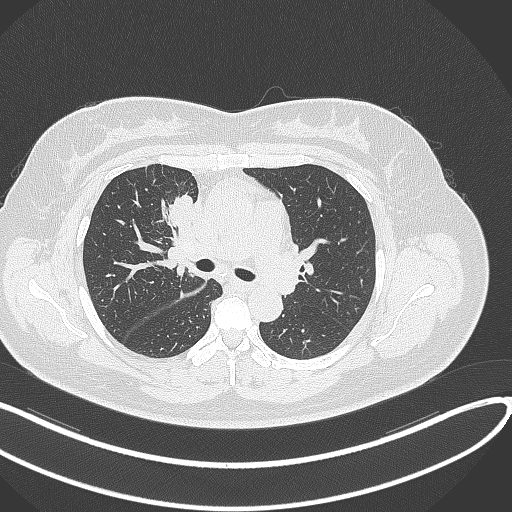
Chest CT, one axial slice. Slice 172 of 303 in the series (ordered by position). Reconstruction kernel B70f. Lung window (W 1500 / L -600 HU). 512 × 512 image matrix, field of view 400 × 400 mm. Patient: female, 46 years. Case-level facts recorded for this patient, not image findings: clinical TNM (as recorded): T2a N1 M0.
Annotated regions visible in this slice (rectangle marked by the reading radiologist):
- lung tumour (recorded histology: adenocarcinoma): box from (x=168, y=193) to (x=202, y=239) px